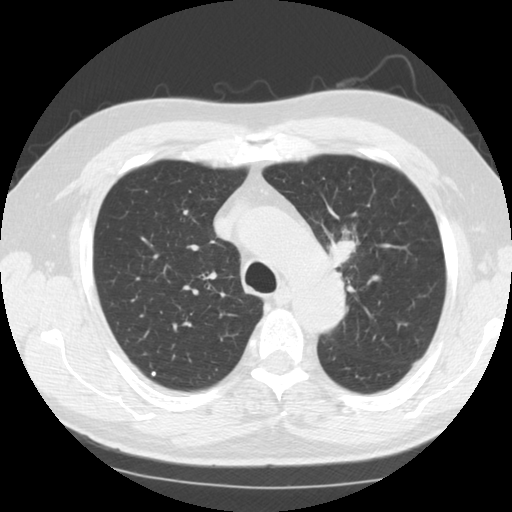
Low-dose screening chest CT, one axial slice; slice 94 of 124 in the series (ordered by position); reconstruction kernel STANDARD; 120 kVp; lung window (W 1500 / L -600 HU); 2.5 mm slice thickness; 512 × 512 image matrix, field of view 340 × 340 mm.
Annotated regions visible in this slice (expert manual segmentation):
- lesion 1 (tumor, upper lobe of left lung): bounding box (x1, y1, x2, y2) in pixels: (329, 239, 355, 268)